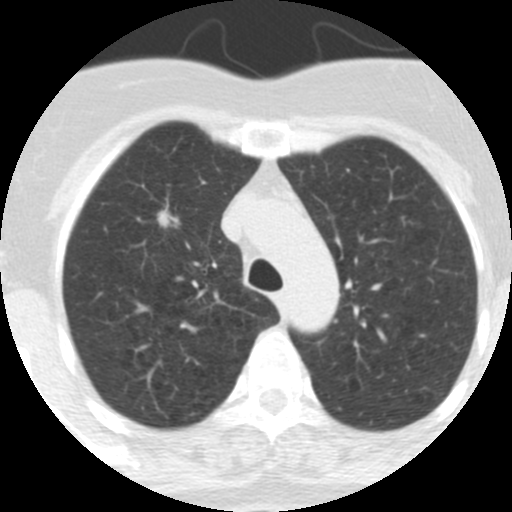
Low-dose screening chest CT, axial slice, baseline annual screen, lung window (W 1500 / L -600 HU), 2.5 mm slice thickness, slice 76 of 313 in the series. Female, age 62 years at enrolment. Current smoker at enrolment.
- Expert reader's lesion annotation, bounding box (x1, y1, x2, y2) in pixels: (116, 160, 181, 233).
- The exam's reader record, not a measurement of the box and not confirmed to be the same lesion: non-calcified nodule or mass ≥4 mm, right upper lobe, 9 × 7 mm, spiculated (stellate) margins, soft tissue attenuation.
- Official screen result: positive, change unspecified: nodule(s) >= 4 mm or enlarging nodule(s), mass(es), or other non-specific abnormalities suspicious for lung cancer.
- Later outcome: lung cancer diagnosed 126 days after this screen — adenocarcinoma, NOS, right upper lobe, moderately differentiated (G2), stage IA (AJCC 6th edition), 18 mm at pathology.